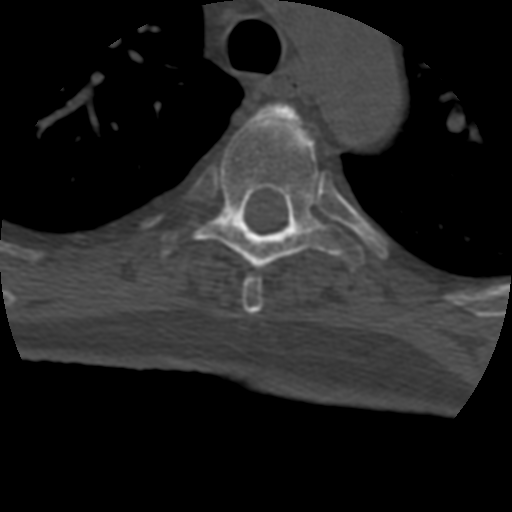
CT including the spine, one axial slice. Slice 321 of 399 in the series (ordered by position). 120 kVp. Bone window (W 1800 / L 400 HU). 512 × 512 image matrix. Patient age 69 years. From the clinical record (not read from this slice): primary cancer: prostate.
Structures marked on this image (semi-automatic segmentation, software-assisted and operator-edited):
- T4 vertebra: bounding box (x1, y1, x2, y2) in pixels: (242, 103, 313, 314)
- T5 vertebra: (164, 105, 364, 270)